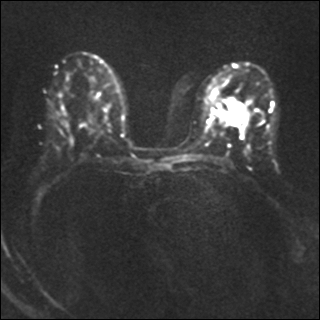
Breast MRI, one axial slice; slice 22 of 40 in the series (ordered by position); diffusion-weighted series; image 2 of 4 stored at this slice position (different b-values; order by instance number); 1.5 T; 4 mm slice thickness; 320 × 320 image matrix. Female patient.
Structures marked on this image (outlined manually by an expert reader):
- tumour on diffusion-weighted imaging: box from (x=230, y=102) to (x=243, y=125) px